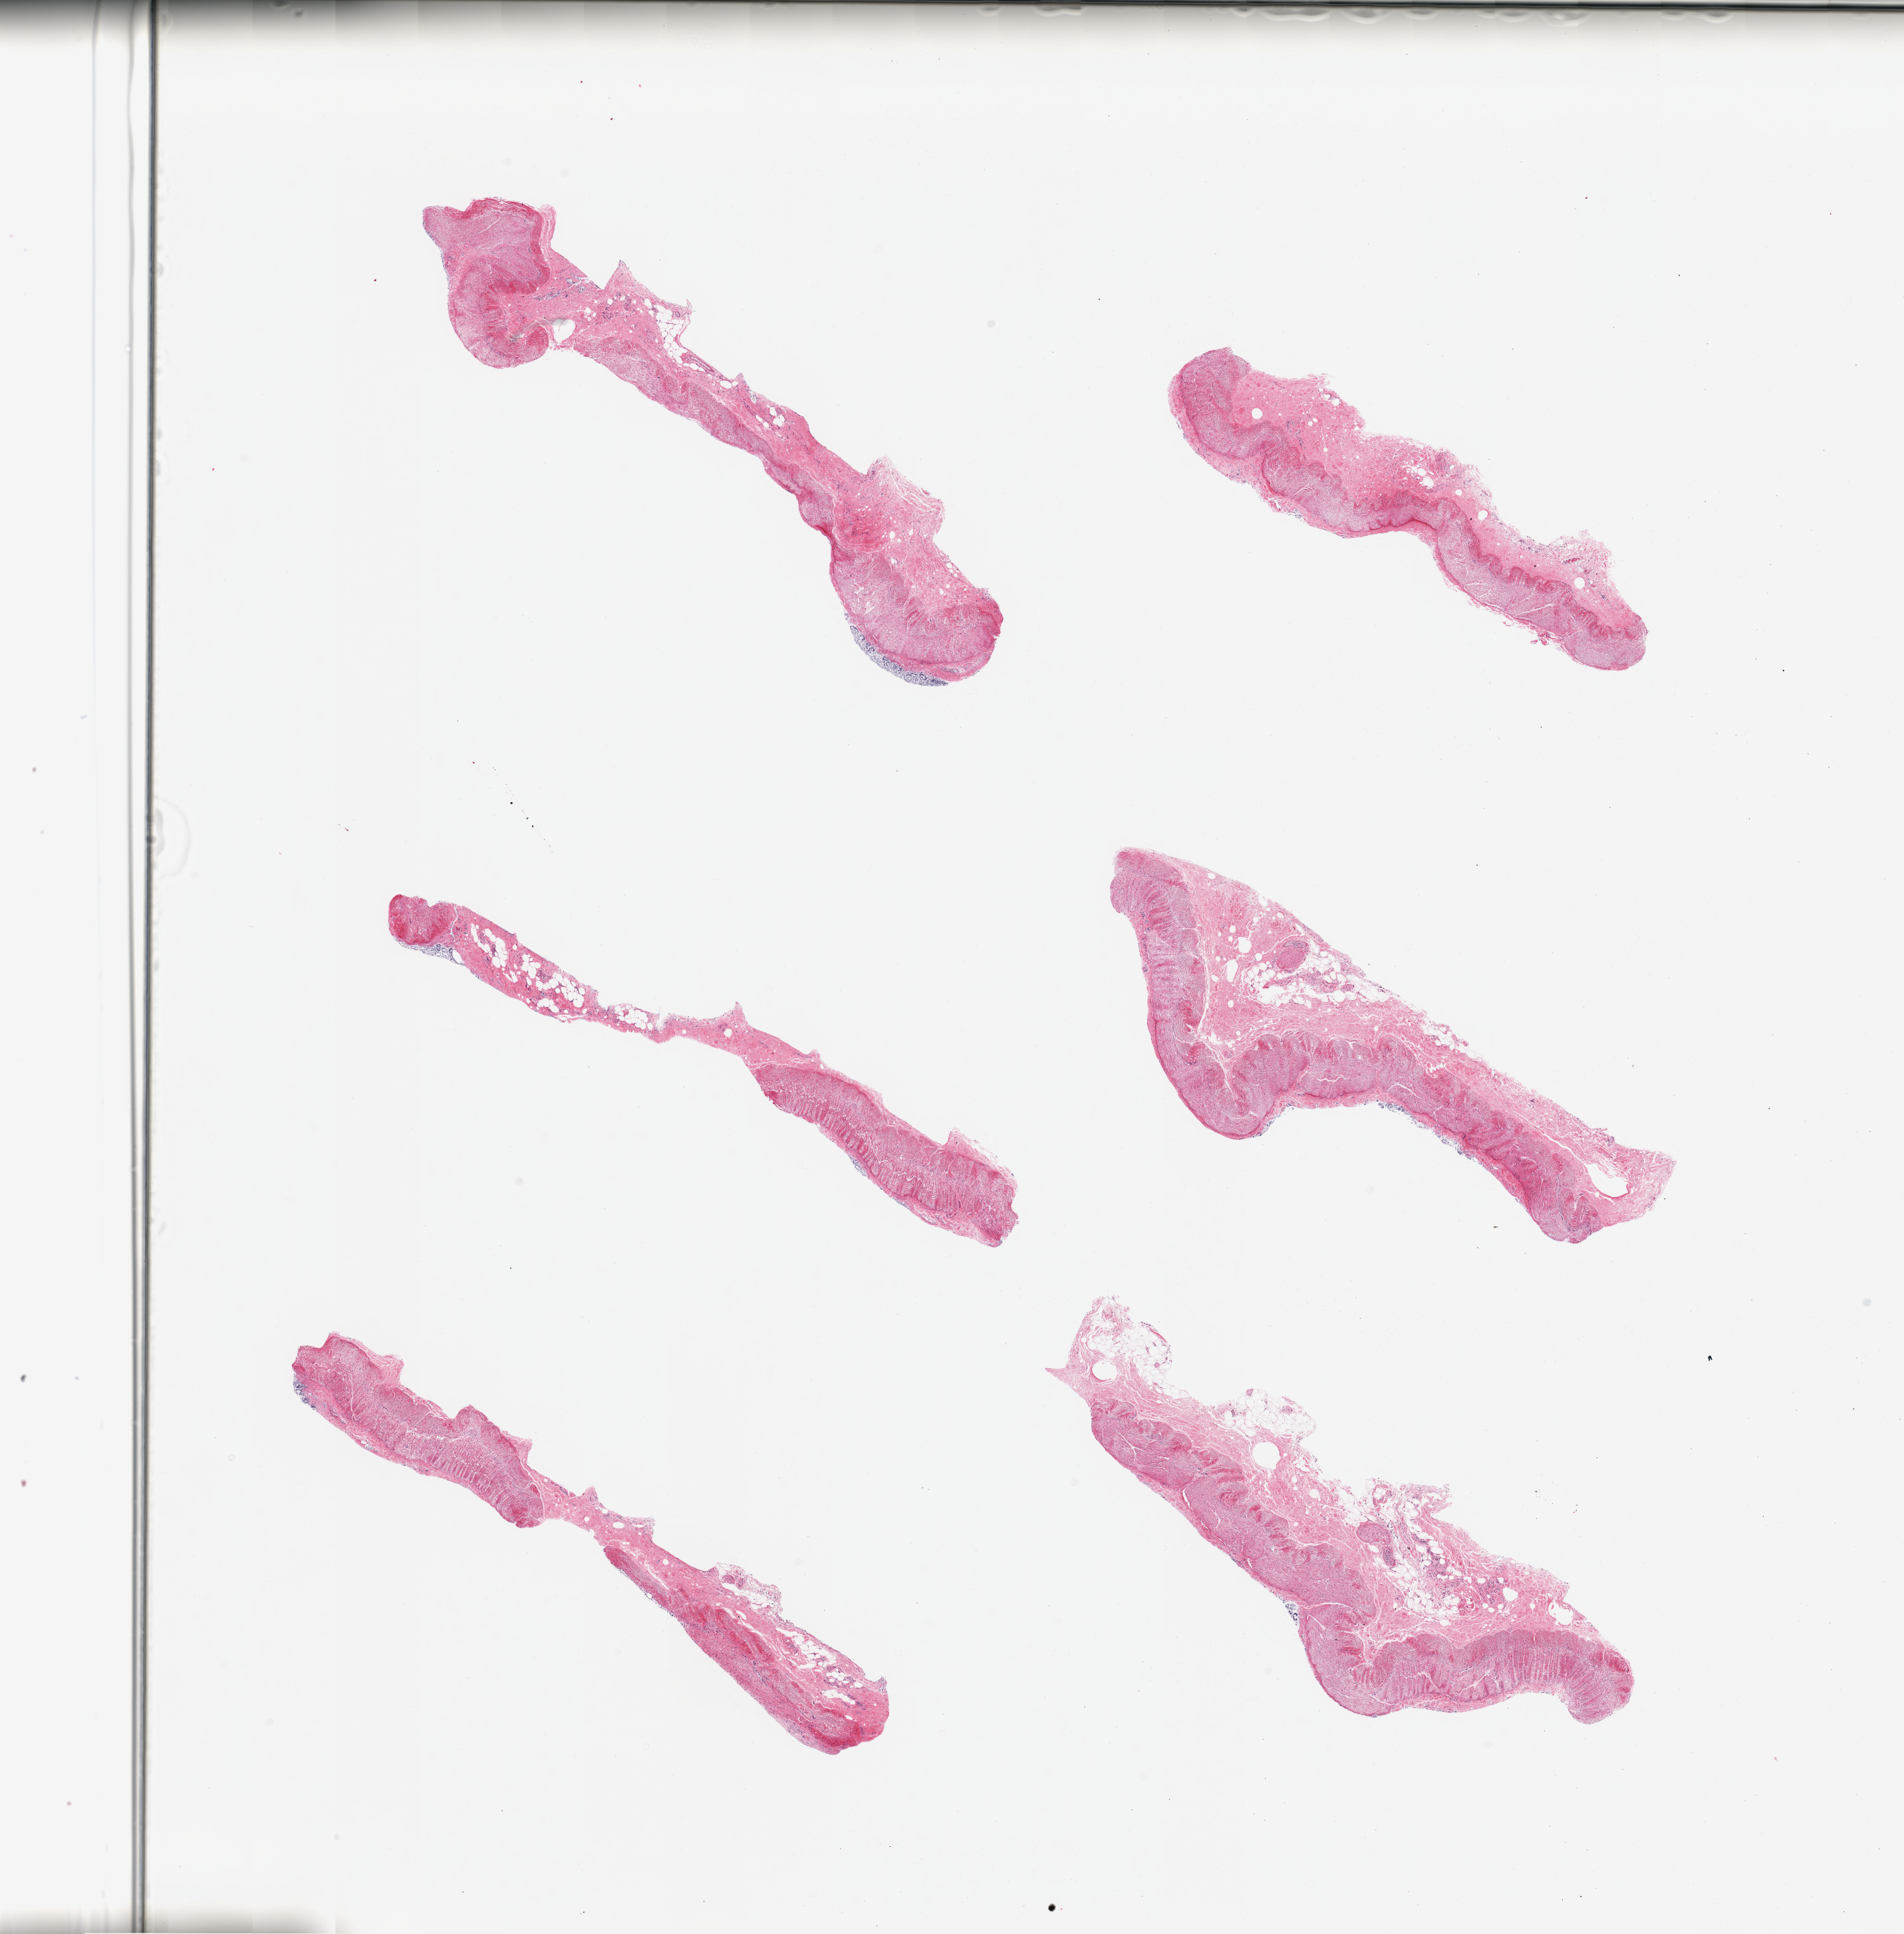
Whole-slide image, hematoxylin and eosin (H&E) stain, a low-resolution overview of the entire scanned area, about 22.6 x 23.0 mm, PAXgene-fixed, paraffin-embedded tissue, section of sigmoid colon (target tissue), donor tissue sample. Donor sex: male.
Pathologist's review note for this sample: 4 pieces; autolyzed small focal rims of mucosa; moderate to severe autolysis of target muscularis.